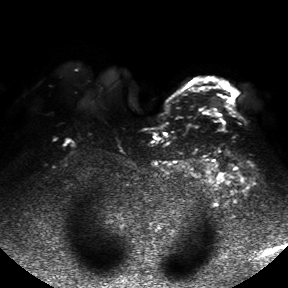
Breast MRI, one axial slice. Slice 37 of 50 in the series (ordered by position). Diffusion-weighted series; image 2 of 4 stored at this slice position (different b-values; order by instance number). 1.5 T. 288 × 288 image matrix, field of view 390 × 390 mm. Female patient.
Outlined on this slice (manually delineated by an expert):
- tumour on diffusion-weighted imaging: bounding box [x1, y1, x2, y2] px = [208, 109, 218, 118]